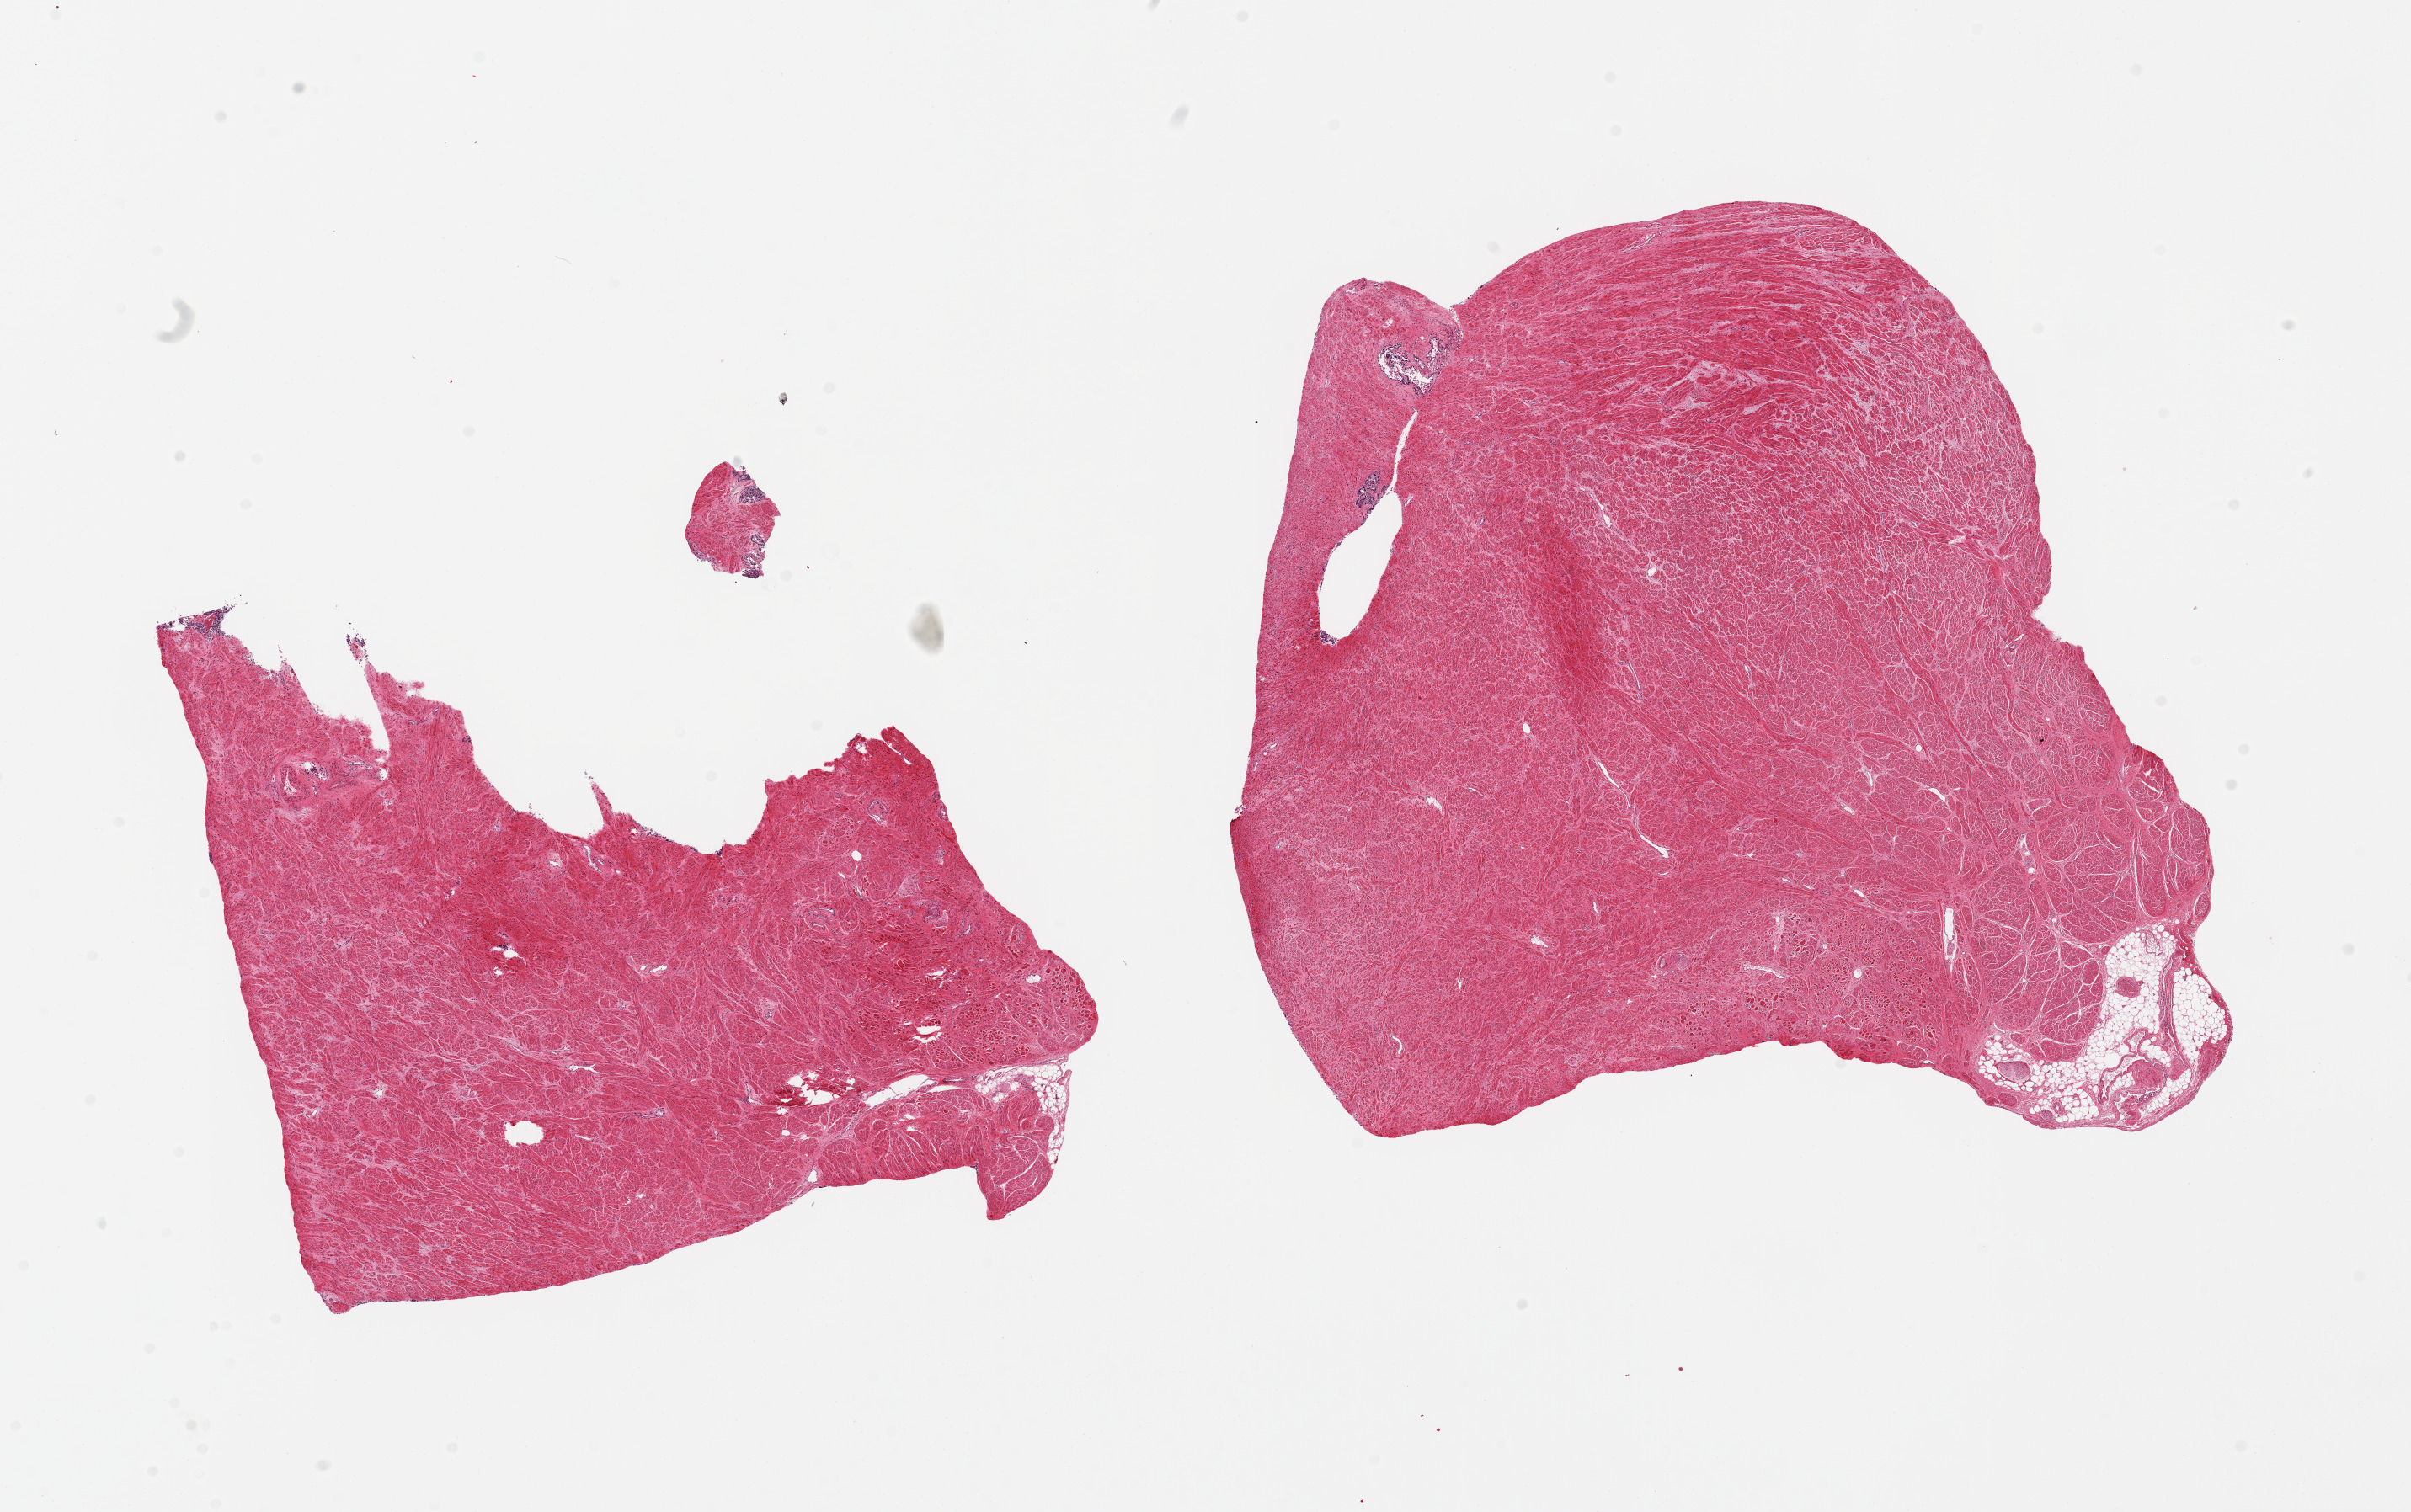
Whole-slide image, hematoxylin and eosin (H&E) stain — shown as a low-resolution overview of the whole scanned area (about 22.6 x 14.2 mm, acquisition: 20x scan). PAXgene-fixed paraffin-embedded (PFPE) section. Section of prostate (target tissue). Donor tissue sample.
* reviewer comment on this tissue sample: 2 pieces, 8x7 & 10x9mm; all stroma